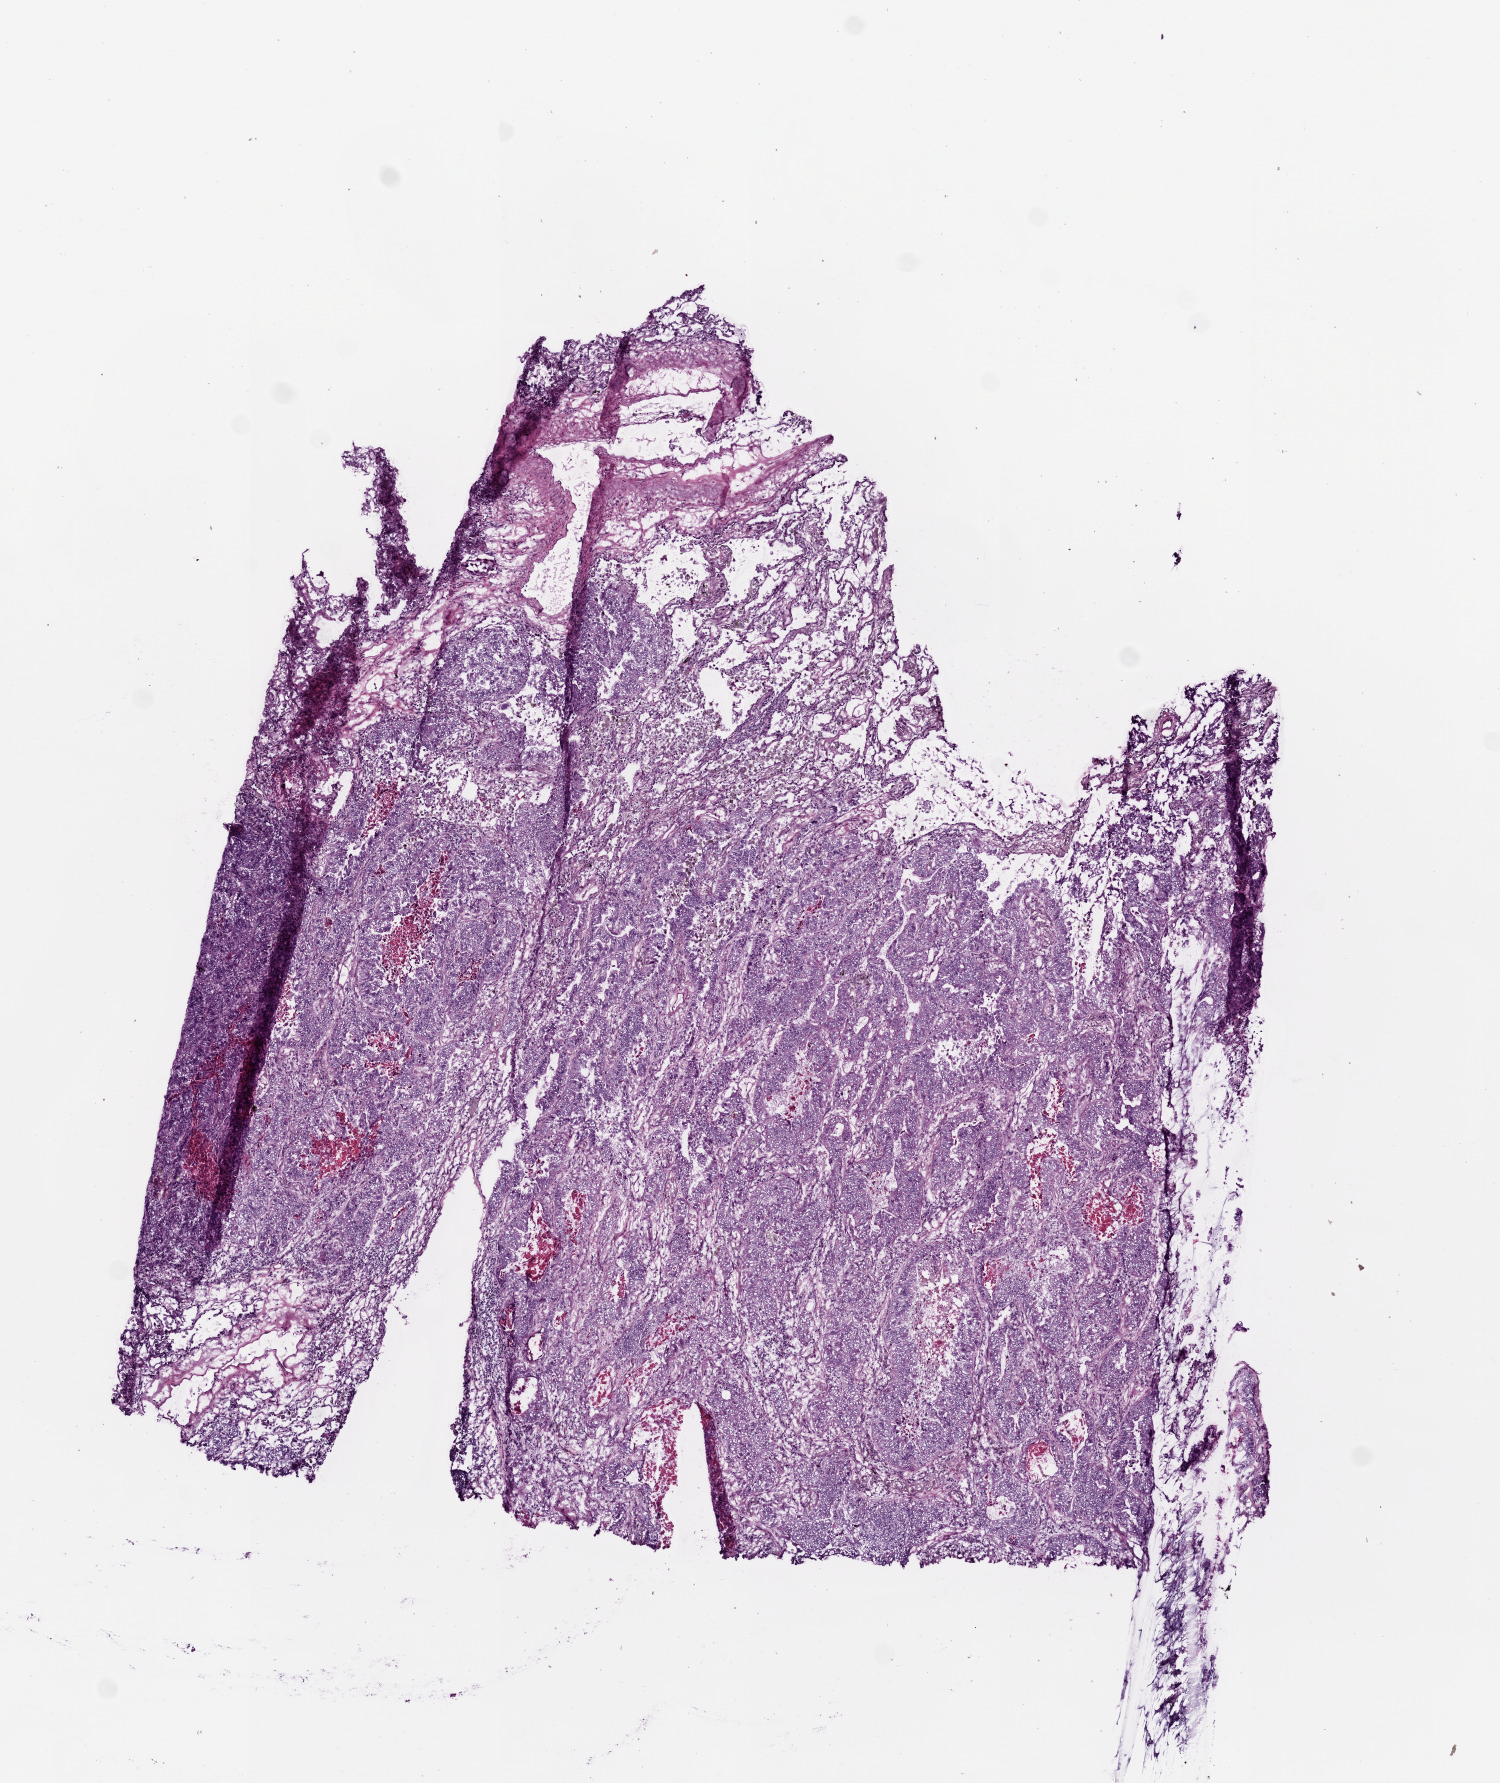
Hematoxylin and eosin (H&E) stained whole-slide image, whole scanned area (about 6.0 x 7.2 mm, from a 20x scan) shown as a low-resolution overview; frozen section; lung, primary tumour sample. Patient: male, age at initial diagnosis 70 years. Composition of this section per pathologist review: tumour cells 85%, tumour nuclei 80%, normal cells 5%, stromal cells 5%, necrosis 5%.
Pathologic diagnosis: Adenocarcinoma with mixed subtypes (upper lobe, lung). AJCC pathologic stage: IIB. Laterality: right.